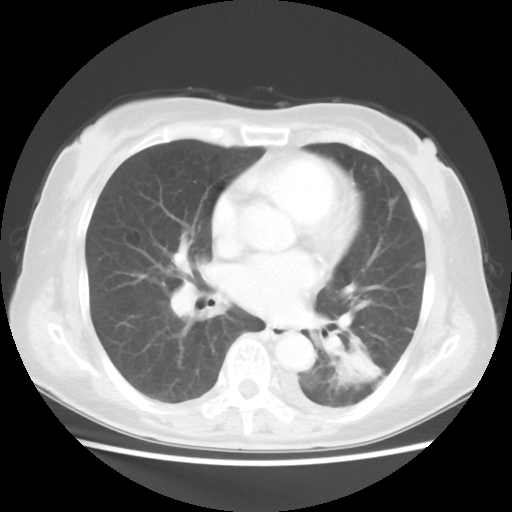
Chest CT, one axial slice; slice 17 of 40 in the series (ordered by position); reconstruction kernel STANDARD; 100 kVp; lung window (W 1500 / L -600 HU); 512 × 512 image matrix. Female patient, age 69 years. From the clinical record (not read from this slice): clinical TNM (as recorded): T1c N0 M0.
Outlined on this slice (rectangle marked by the reading radiologist):
- lung tumour (recorded histology: adenocarcinoma): box from (x=339, y=341) to (x=380, y=392) px